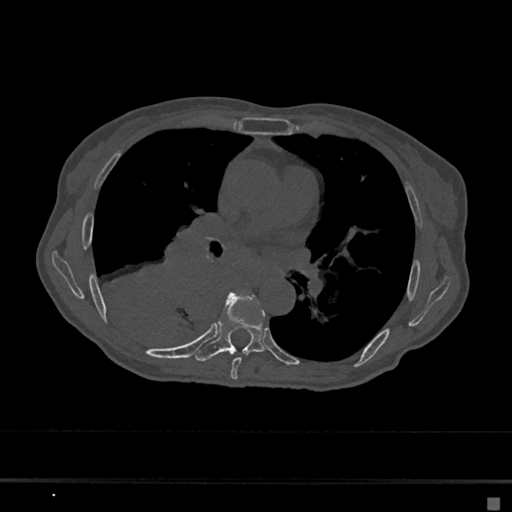
CT including the spine, one axial slice; slice 390 of 797 in the series (ordered by position); reconstruction kernel Br40s/3; 120 kVp; bone window (W 1800 / L 400 HU); 512 × 512 image matrix, field of view 360 × 360 mm. Female patient, age 68 years. From the clinical record (not read from this slice): primary cancer: renal.
Annotated regions visible in this slice (semi-automatically segmented with operator editing):
- T6 vertebra: bounding box [x1, y1, x2, y2] px = [230, 309, 264, 379]
- T7 vertebra: [195, 292, 264, 362]